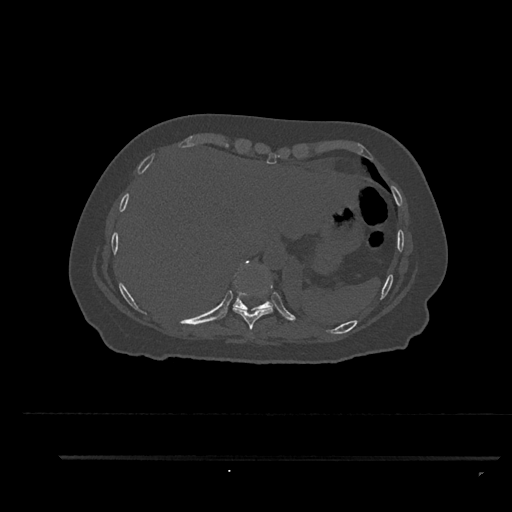
CT including the spine, one axial slice; slice 395 of 797 in the series (ordered by position); reconstruction kernel Br40s/3; 120 kVp; bone window (W 1800 / L 400 HU); 0.5 mm slice thickness; 512 × 512 image matrix, field of view 408 × 408 mm. Female patient, age 44 years. From the clinical record (not read from this slice): primary cancer: renal.
Outlined on this slice (semi-automatic segmentation, software-assisted and operator-edited):
- T10 vertebra: bounding box <233,260,274,311> (left, top, right, bottom; pixels)
- T8 vertebra: <249,332,253,334>
- T9 vertebra: <233,307,273,330>